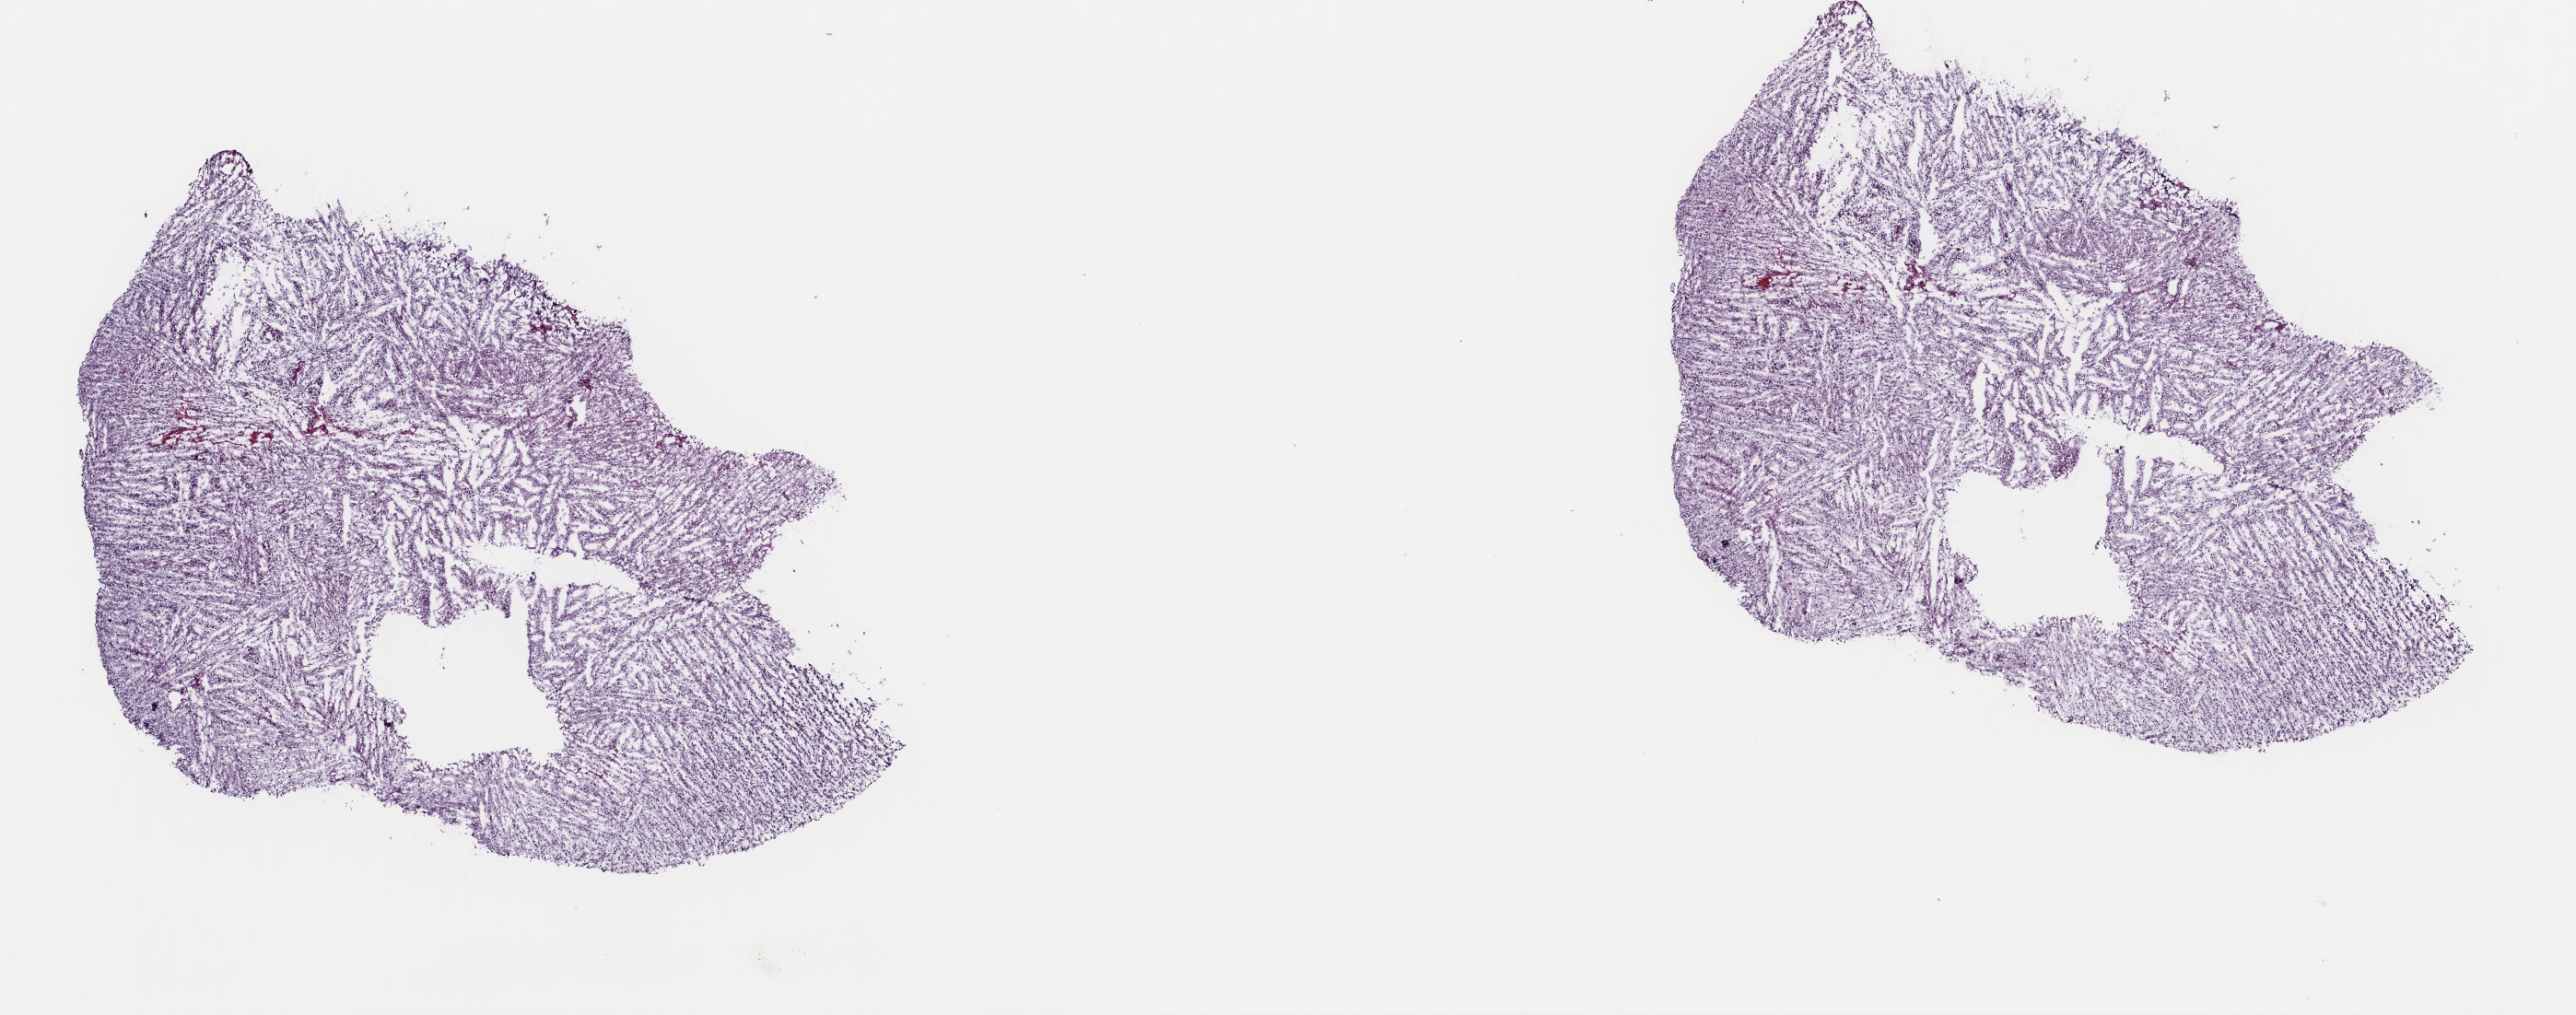
Whole-slide histology image, Hematoxylin and eosin (H&E) stained — low-resolution overview of the scanned area, about 22.1 x 8.7 mm. Frozen section from the top of the tissue portion. Recurrent tumour sample from the brain. Male patient; age at initial diagnosis 70 years. Slide review estimates, as recorded: tumour cells 80%, tumour nuclei 85%, normal cells 10%, stromal cells 10%, necrosis 0%. Infiltration values recorded for this section: lymphocyte infiltration 0%, monocyte infiltration 0%, neutrophil infiltration 0%.
- this section: recurrent tumour
- patient diagnosis: Oligodendroglioma, anaplastic (cerebrum)